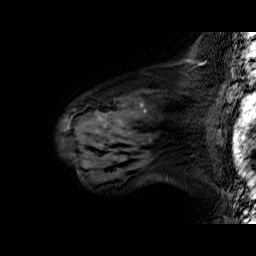
Breast MRI (dynamic contrast-enhanced), one sagittal slice. Slice 45 of 60 in the series (ordered by position). Dynamic contrast-enhanced series, time point 2 of 6 at this slice position (early post-contrast). 1.5 T. TE 6.4 ms, TR 32.9 ms. 256 × 256 image matrix, field of view 200 × 200 mm. Female patient. From the clinical record (not read from this slice): setting: breast cancer imaged before/during neoadjuvant chemotherapy; receptor status: HER2-positive.
Annotated regions visible in this slice (semi-automatic segmentation, software-assisted and operator-edited):
- analysis volume of interest (the breast-tissue region the enhancement analysis was run in; not a lesion): bounding box <60,79,196,160> (left, top, right, bottom; pixels)
- tumour enhancement mask (voxels above the 100 % enhancement threshold inside the analysis volume of interest): <67,103,146,129>